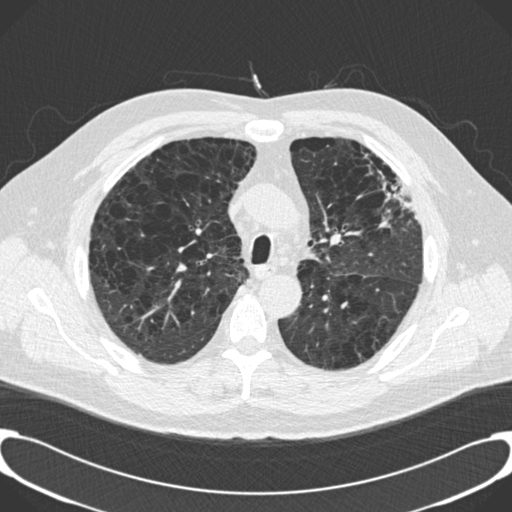
Low-dose screening chest CT, one axial slice. Slice 142 of 189 in the series (ordered by position). Reconstruction kernel B30f. 120 kVp. Lung window (W 1500 / L -600 HU). 512 × 512 image matrix, field of view 380 × 380 mm.
Annotated regions visible in this slice (manually delineated by an expert):
- lesion 1 (tumor, upper lobe of left lung): box from (x=387, y=179) to (x=417, y=219) px